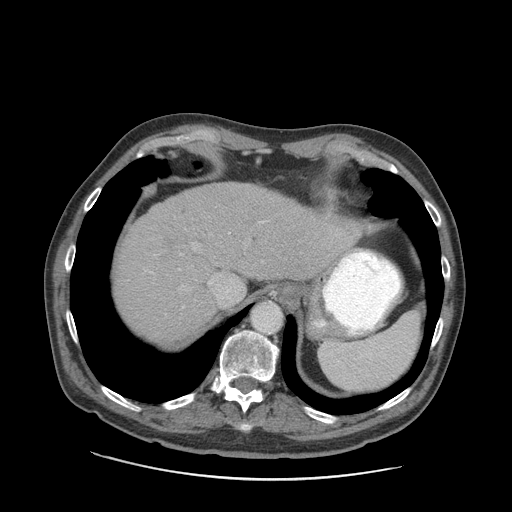
Contrast-enhanced abdominal CT (liver protocol), one axial slice. Slice 72 of 89 in the series (ordered by position). Reconstruction kernel STANDARD. 140 kVp. Soft-tissue window (W 400 / L 40 HU). 2.5 mm slice thickness. 512 × 512 image matrix, field of view 420 × 420 mm. From the clinical record (not read from this slice): diagnosis: hepatocellular carcinoma (patient treated with transarterial chemoembolisation; whether this scan precedes or follows treatment is not stated here); TNM stage (as recorded): Stage-I; Child-Pugh class: A; tumour nodularity: uninodular.
Annotated regions visible in this slice (semi-automatic segmentation, software-assisted and operator-edited):
- liver parenchyma outside the tumour (the mass and vessels are separate outlines, so this box may not span the whole liver): bounding box [x1, y1, x2, y2] px = [114, 182, 362, 342]
- liver vessels: [145, 220, 338, 308]